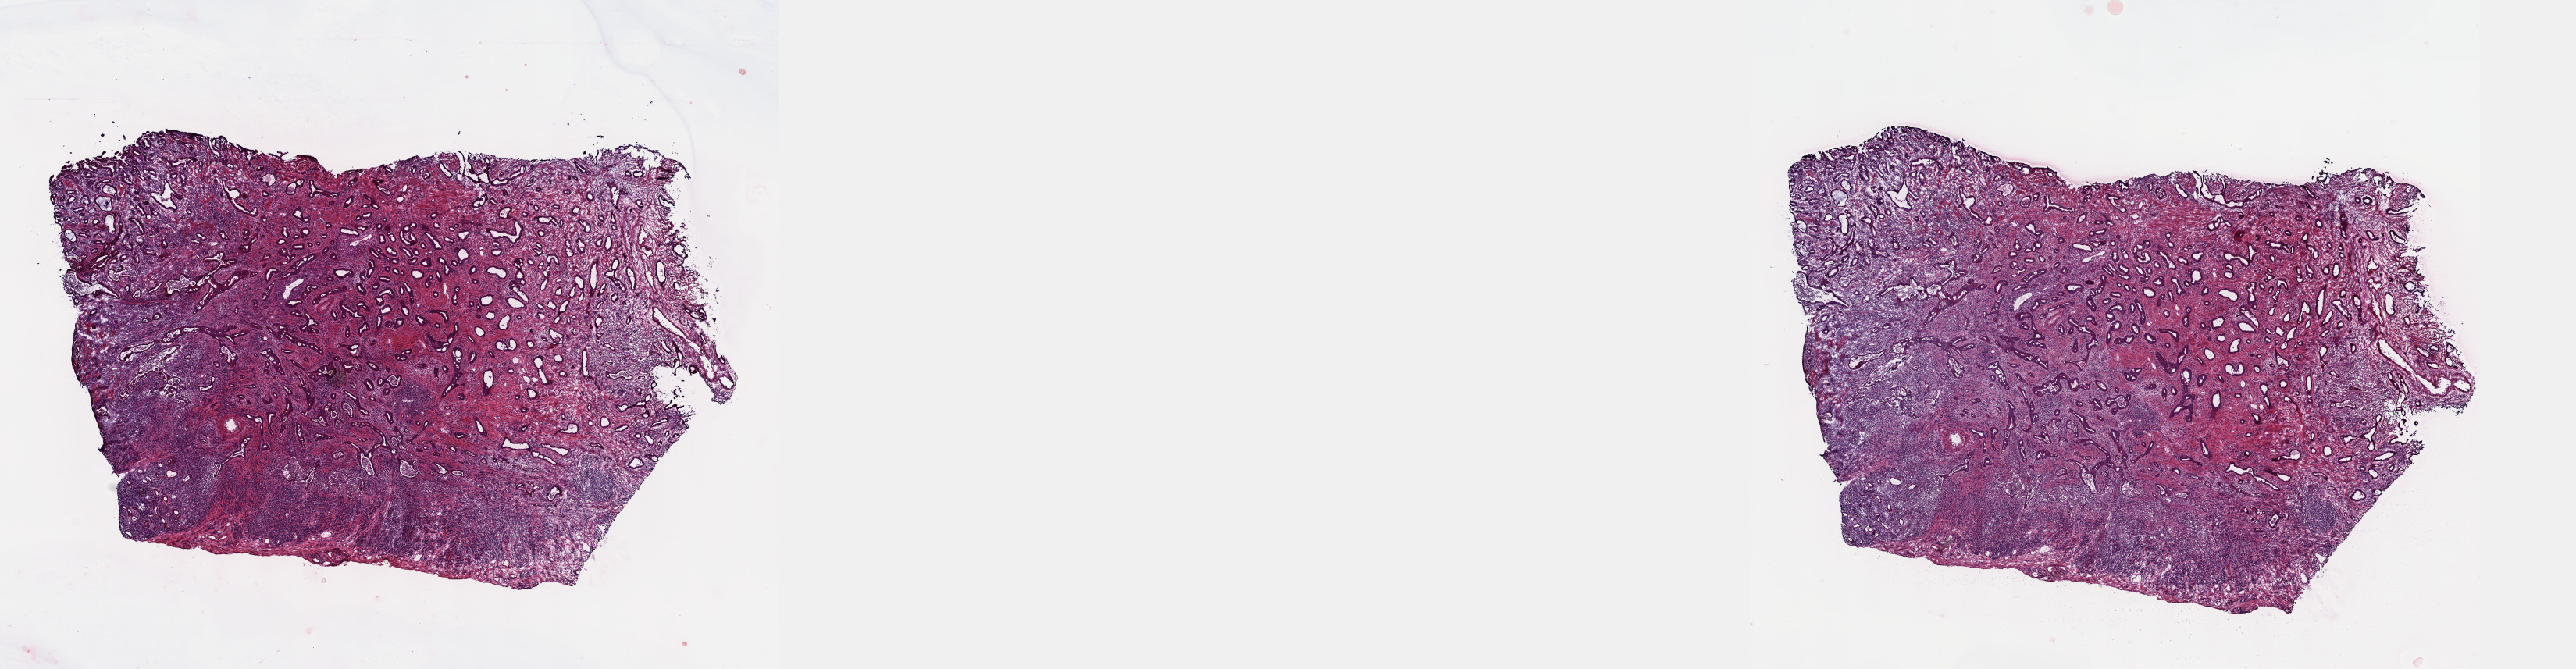
Whole-slide histology image, H&E — low-resolution overview of the scanned area, about 26.7 x 6.9 mm (slide scanned at 40x); frozen section from the top of the tissue portion; primary tumour sample from the esophagus. Male, age 69 years at initial diagnosis. Histologic grade: G1 (well differentiated). Composition of this section per pathologist review: tumour cells 70%, tumour nuclei 70%, normal cells 0%, stromal cells 30%, necrosis 0%. Infiltration values recorded for this section: lymphocyte infiltration 40%, monocyte infiltration 20%, neutrophil infiltration 20%.
• lymph nodes positive (case pathology): 0 of 26 examined
• histologic diagnosis: Adenocarcinoma, NOS (lower third of esophagus)